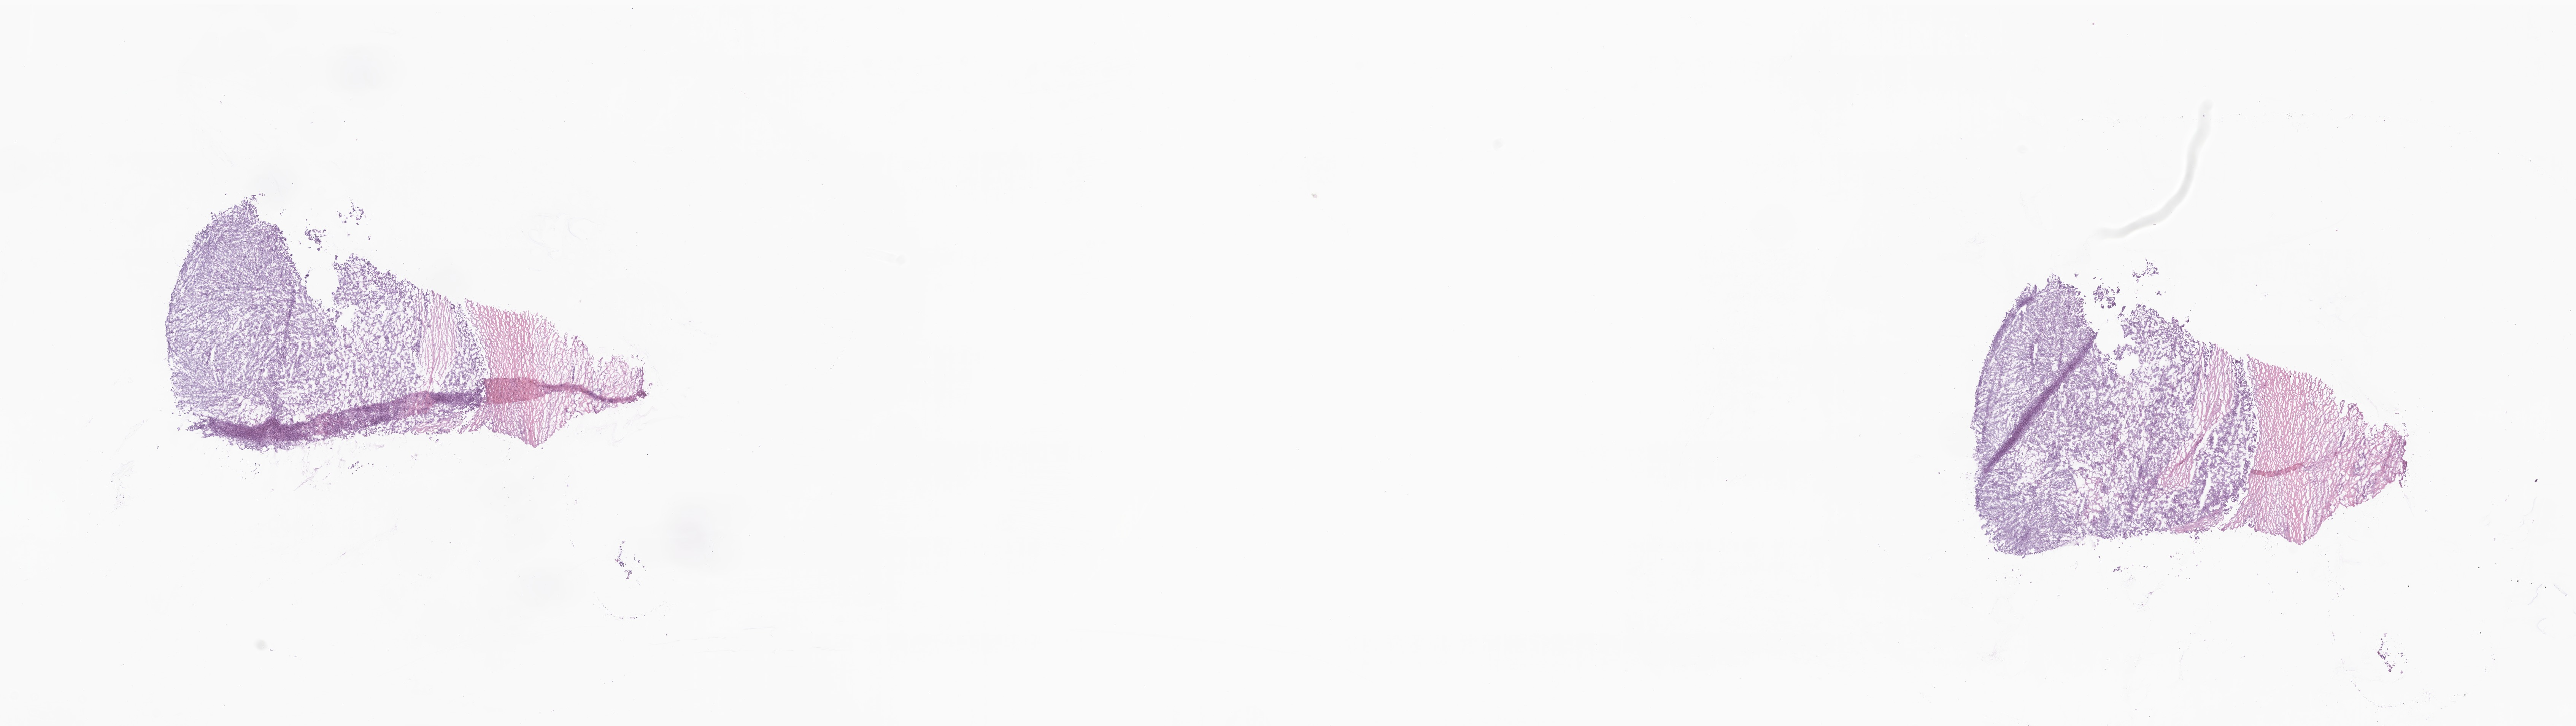
Hematoxylin and eosin (H&E) whole-slide image, a low-resolution overview of the entire scanned area, about 28.6 x 8.0 mm. Cryosection. Metastatic tumor tissue. Patient sex: female. Pathologist review of this section (percent, as recorded): tumor cells 95%, tumor nuclei 96%, stromal cells 0%, necrosis 5%, normal cells 0%. Inflammatory infiltration, as recorded: lymphocyte infiltration 0%, monocyte infiltration 0%, neutrophil infiltration 0%.
Patient diagnosis (primary): Serous surface papillary carcinoma.